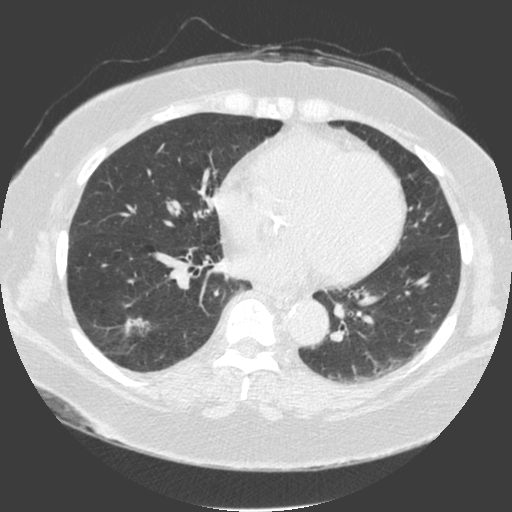
Low-dose screening chest CT, one axial slice; slice 80 of 175 in the series (ordered by position); 120 kVp; lung window (W 1500 / L -600 HU); 2 mm slice thickness; 512 × 512 image matrix.
Structures marked on this image (manually delineated by an expert):
- lesion 1 (tumor, lower lobe of right lung): box from (x=125, y=318) to (x=148, y=333) px